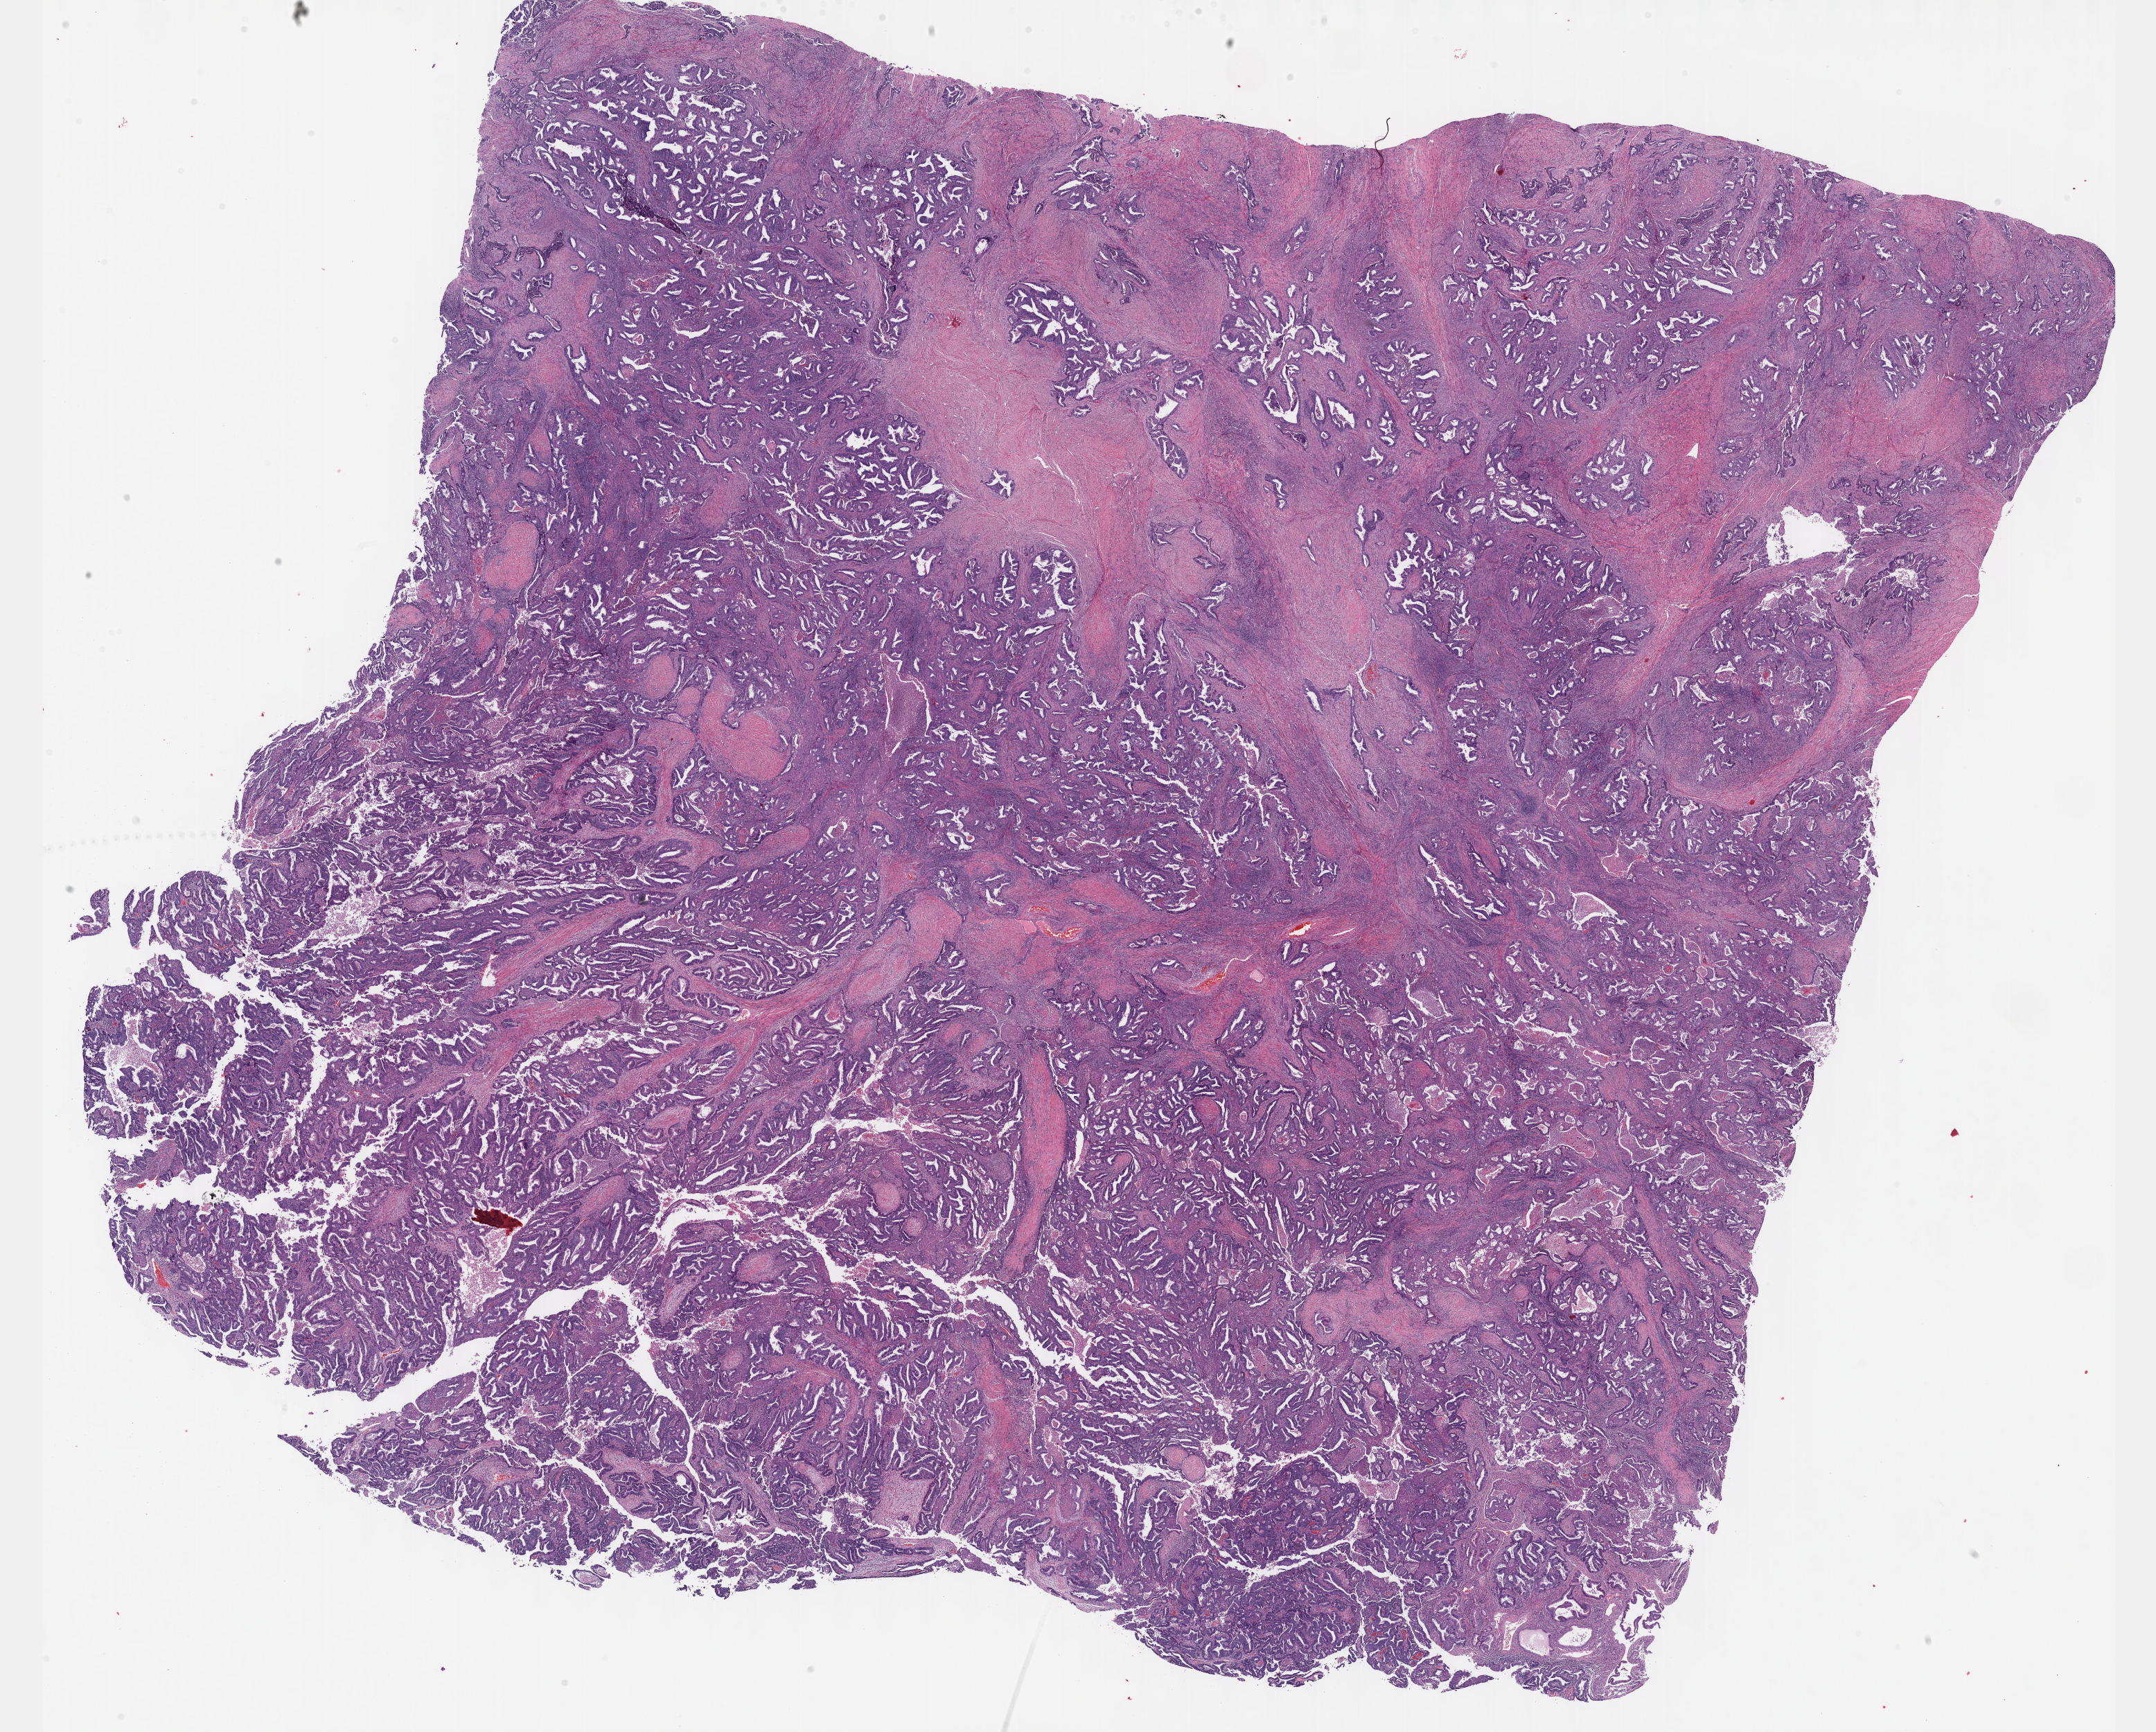
Whole-slide histology image, Hematoxylin and eosin (H&E) stained — shown as a low-resolution overview of the whole scanned area (about 25.1 x 20.2 mm, slide scanned at 40x); FFPE section; primary tumour sample from the uterus. Female, age 51 years at initial diagnosis. Histologic grade: G2 (moderately differentiated).
Histologic diagnosis: Endometrioid adenocarcinoma, NOS. FIGO stage: IIIA. Lymph nodes positive (case pathology): 0 of 5 examined.